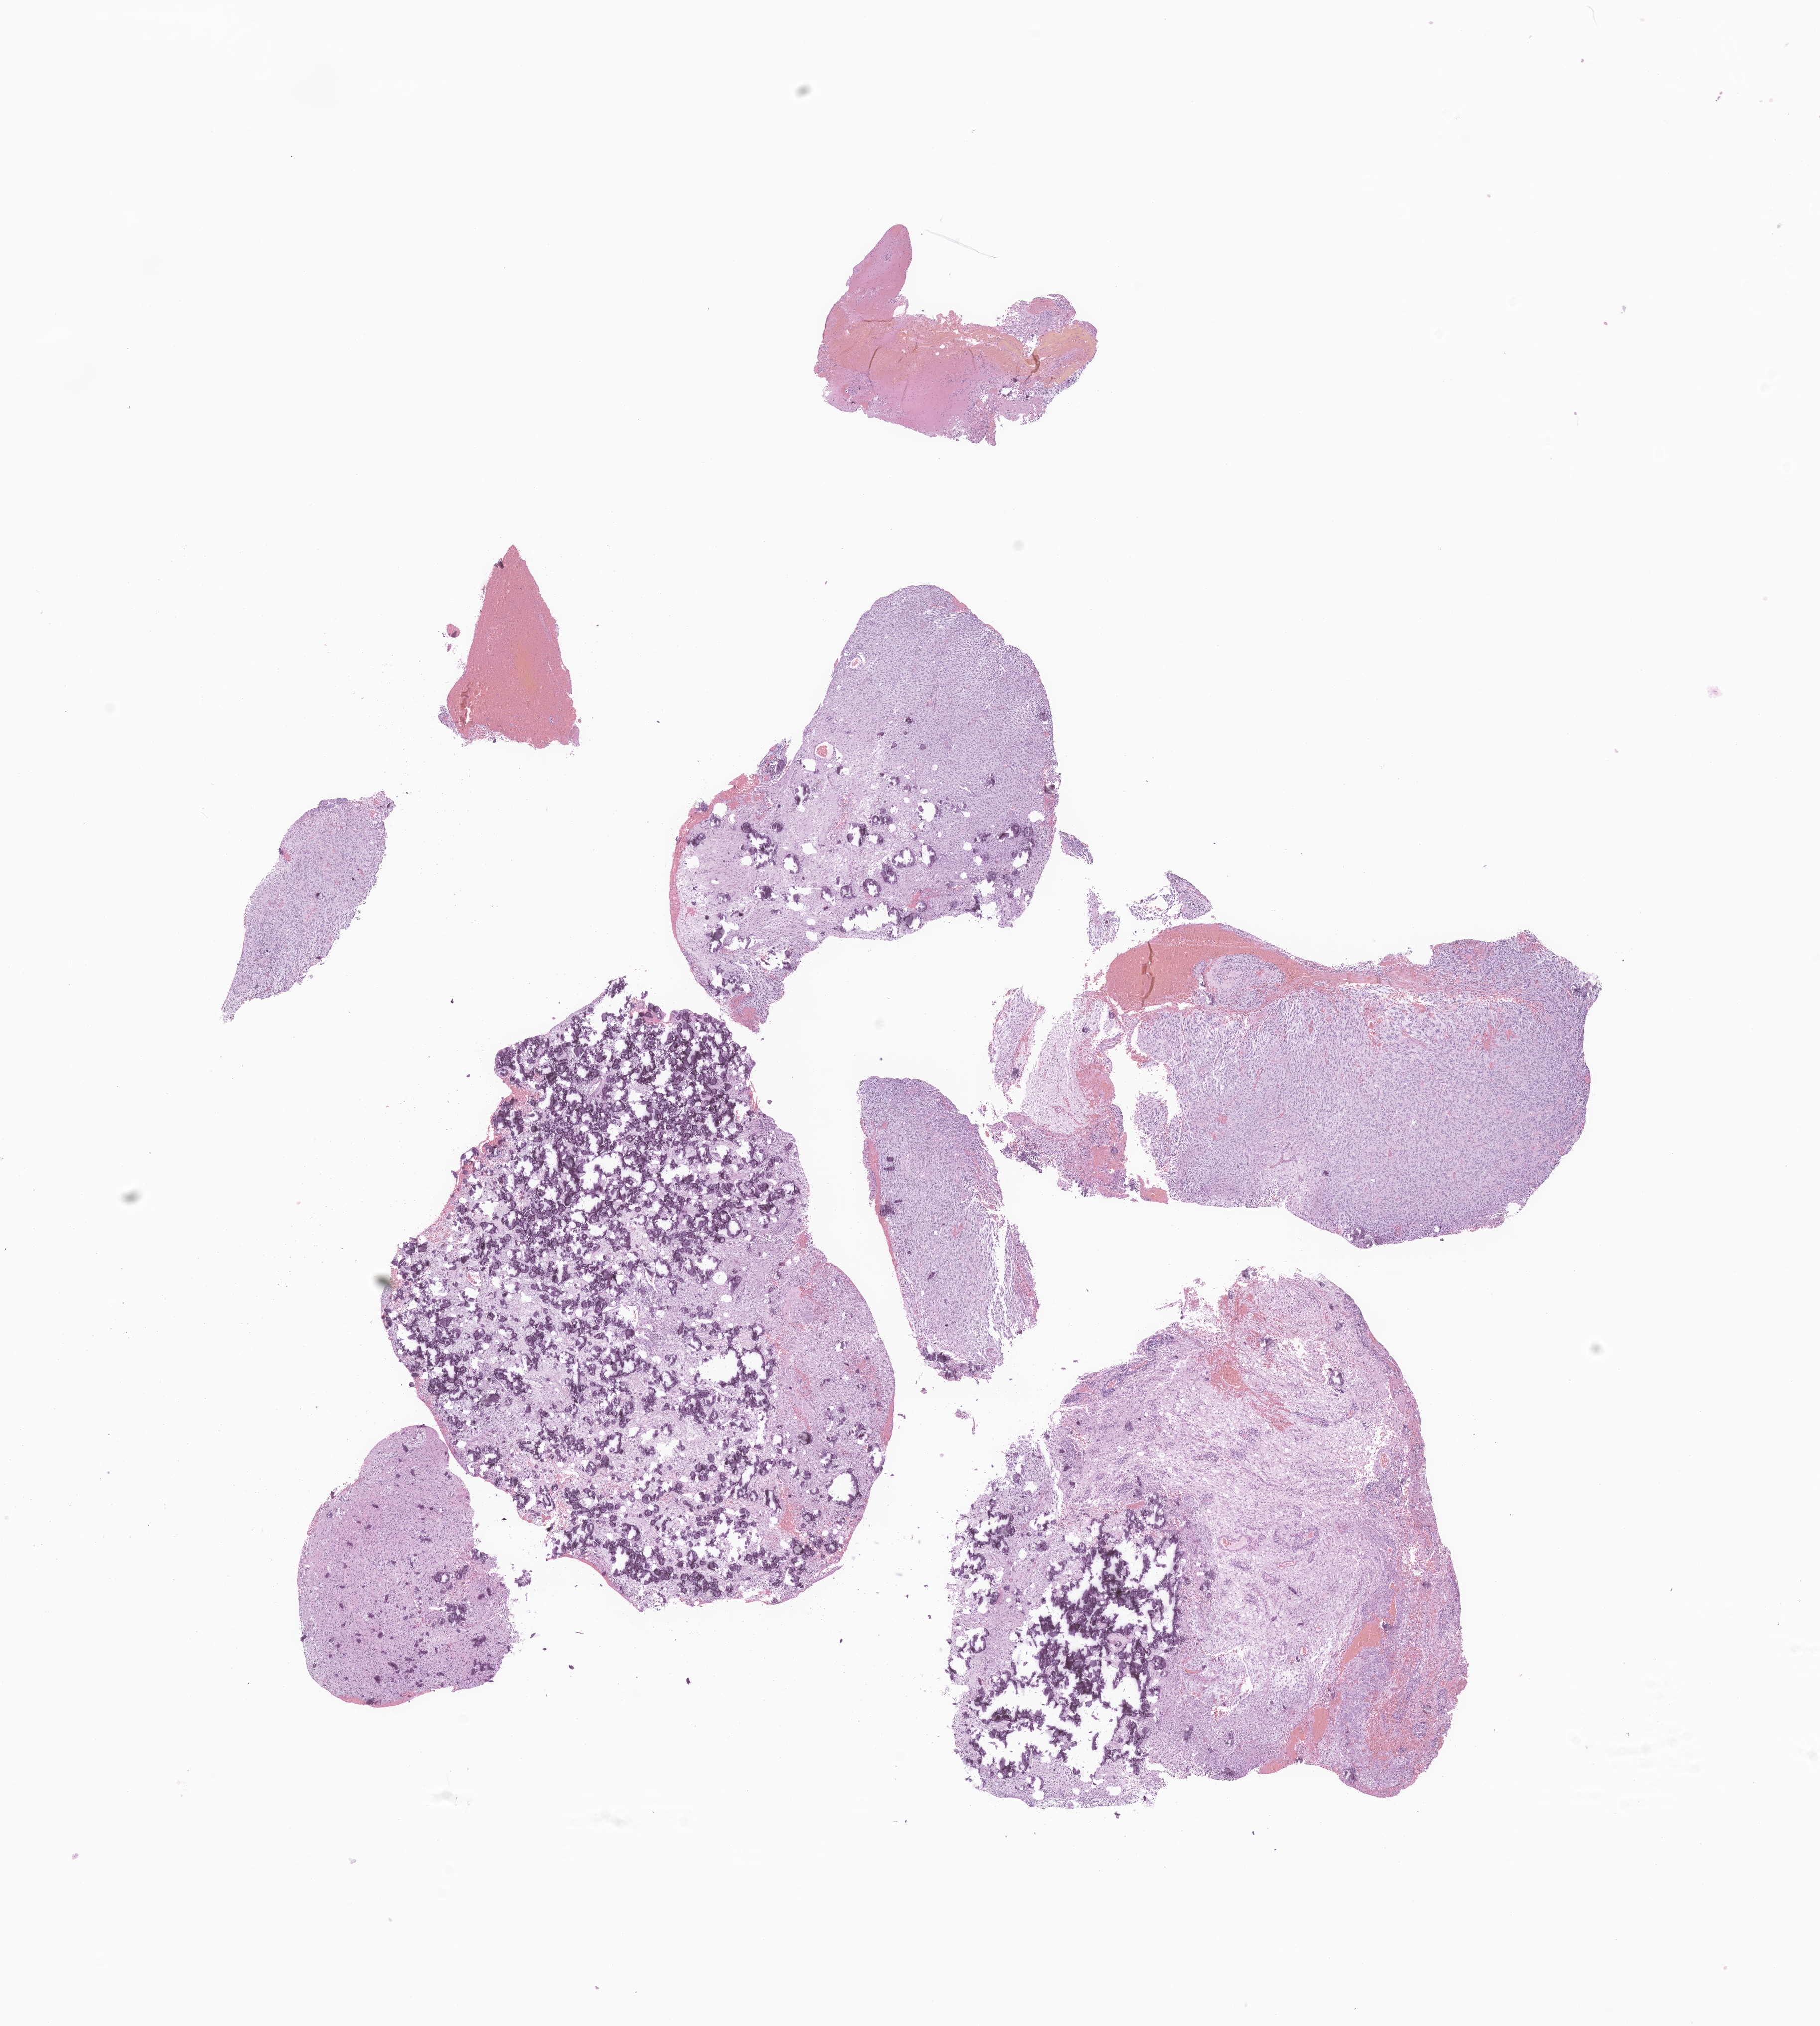
Hematoxylin and eosin (H&E) whole-slide image of tumor tissue from the temporal lobe, shown as a low-resolution overview of the whole scanned area (about 15.4 x 17.1 mm); formalin-fixed paraffin-embedded section. Female patient, age 158 months (13 years 2 months).
Diagnosis (ICD-O-3 morphology term): Ganglioglioma, NOS.